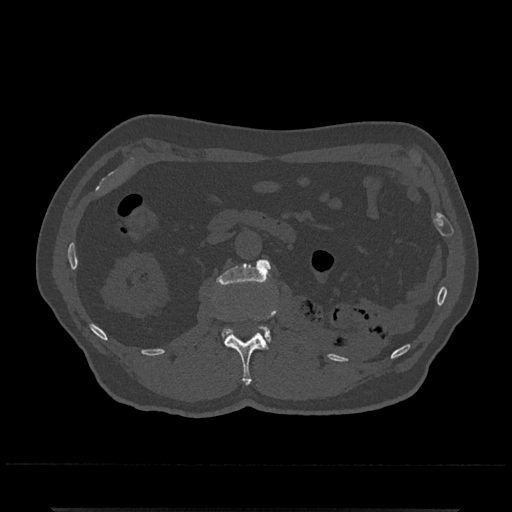
CT including the spine, one axial slice. Slice 334 of 797 in the series (ordered by position). Reconstruction kernel Br40s/3. 120 kVp. Bone window (W 1800 / L 400 HU). 512 × 512 image matrix, field of view 393 × 393 mm. Patient: male, 67 years. From the clinical record (not read from this slice): primary cancer: prostate.
Annotated regions visible in this slice (semi-automatically segmented with operator editing):
- L1 vertebra: box from (x=225, y=309) to (x=277, y=385) px
- L2 vertebra: (x=216, y=259)–(x=271, y=343)